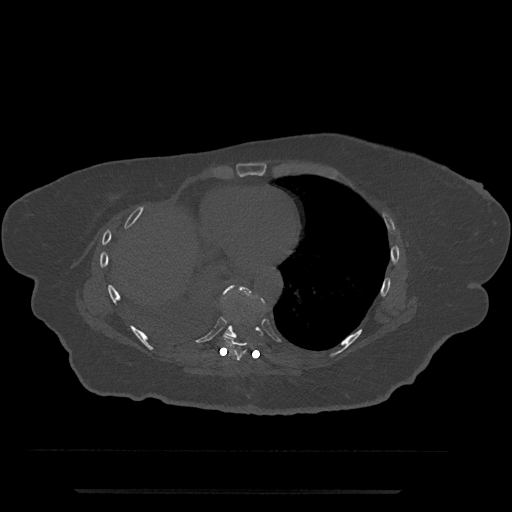
CT including the spine, one axial slice; slice 372 of 797 in the series (ordered by position); reconstruction kernel Br40s/3; 120 kVp; bone window (W 1800 / L 400 HU); 0.5 mm slice thickness; 512 × 512 image matrix. Patient: female, 51 years. From the clinical record (not read from this slice): primary cancer: neuro; vertebrae with lytic lesions (as recorded): T8.
Structures marked on this image (semi-automatically segmented with operator editing):
- T8 vertebra: bounding box [x1, y1, x2, y2] px = [222, 297, 260, 361]
- T9 vertebra: [218, 285, 266, 339]